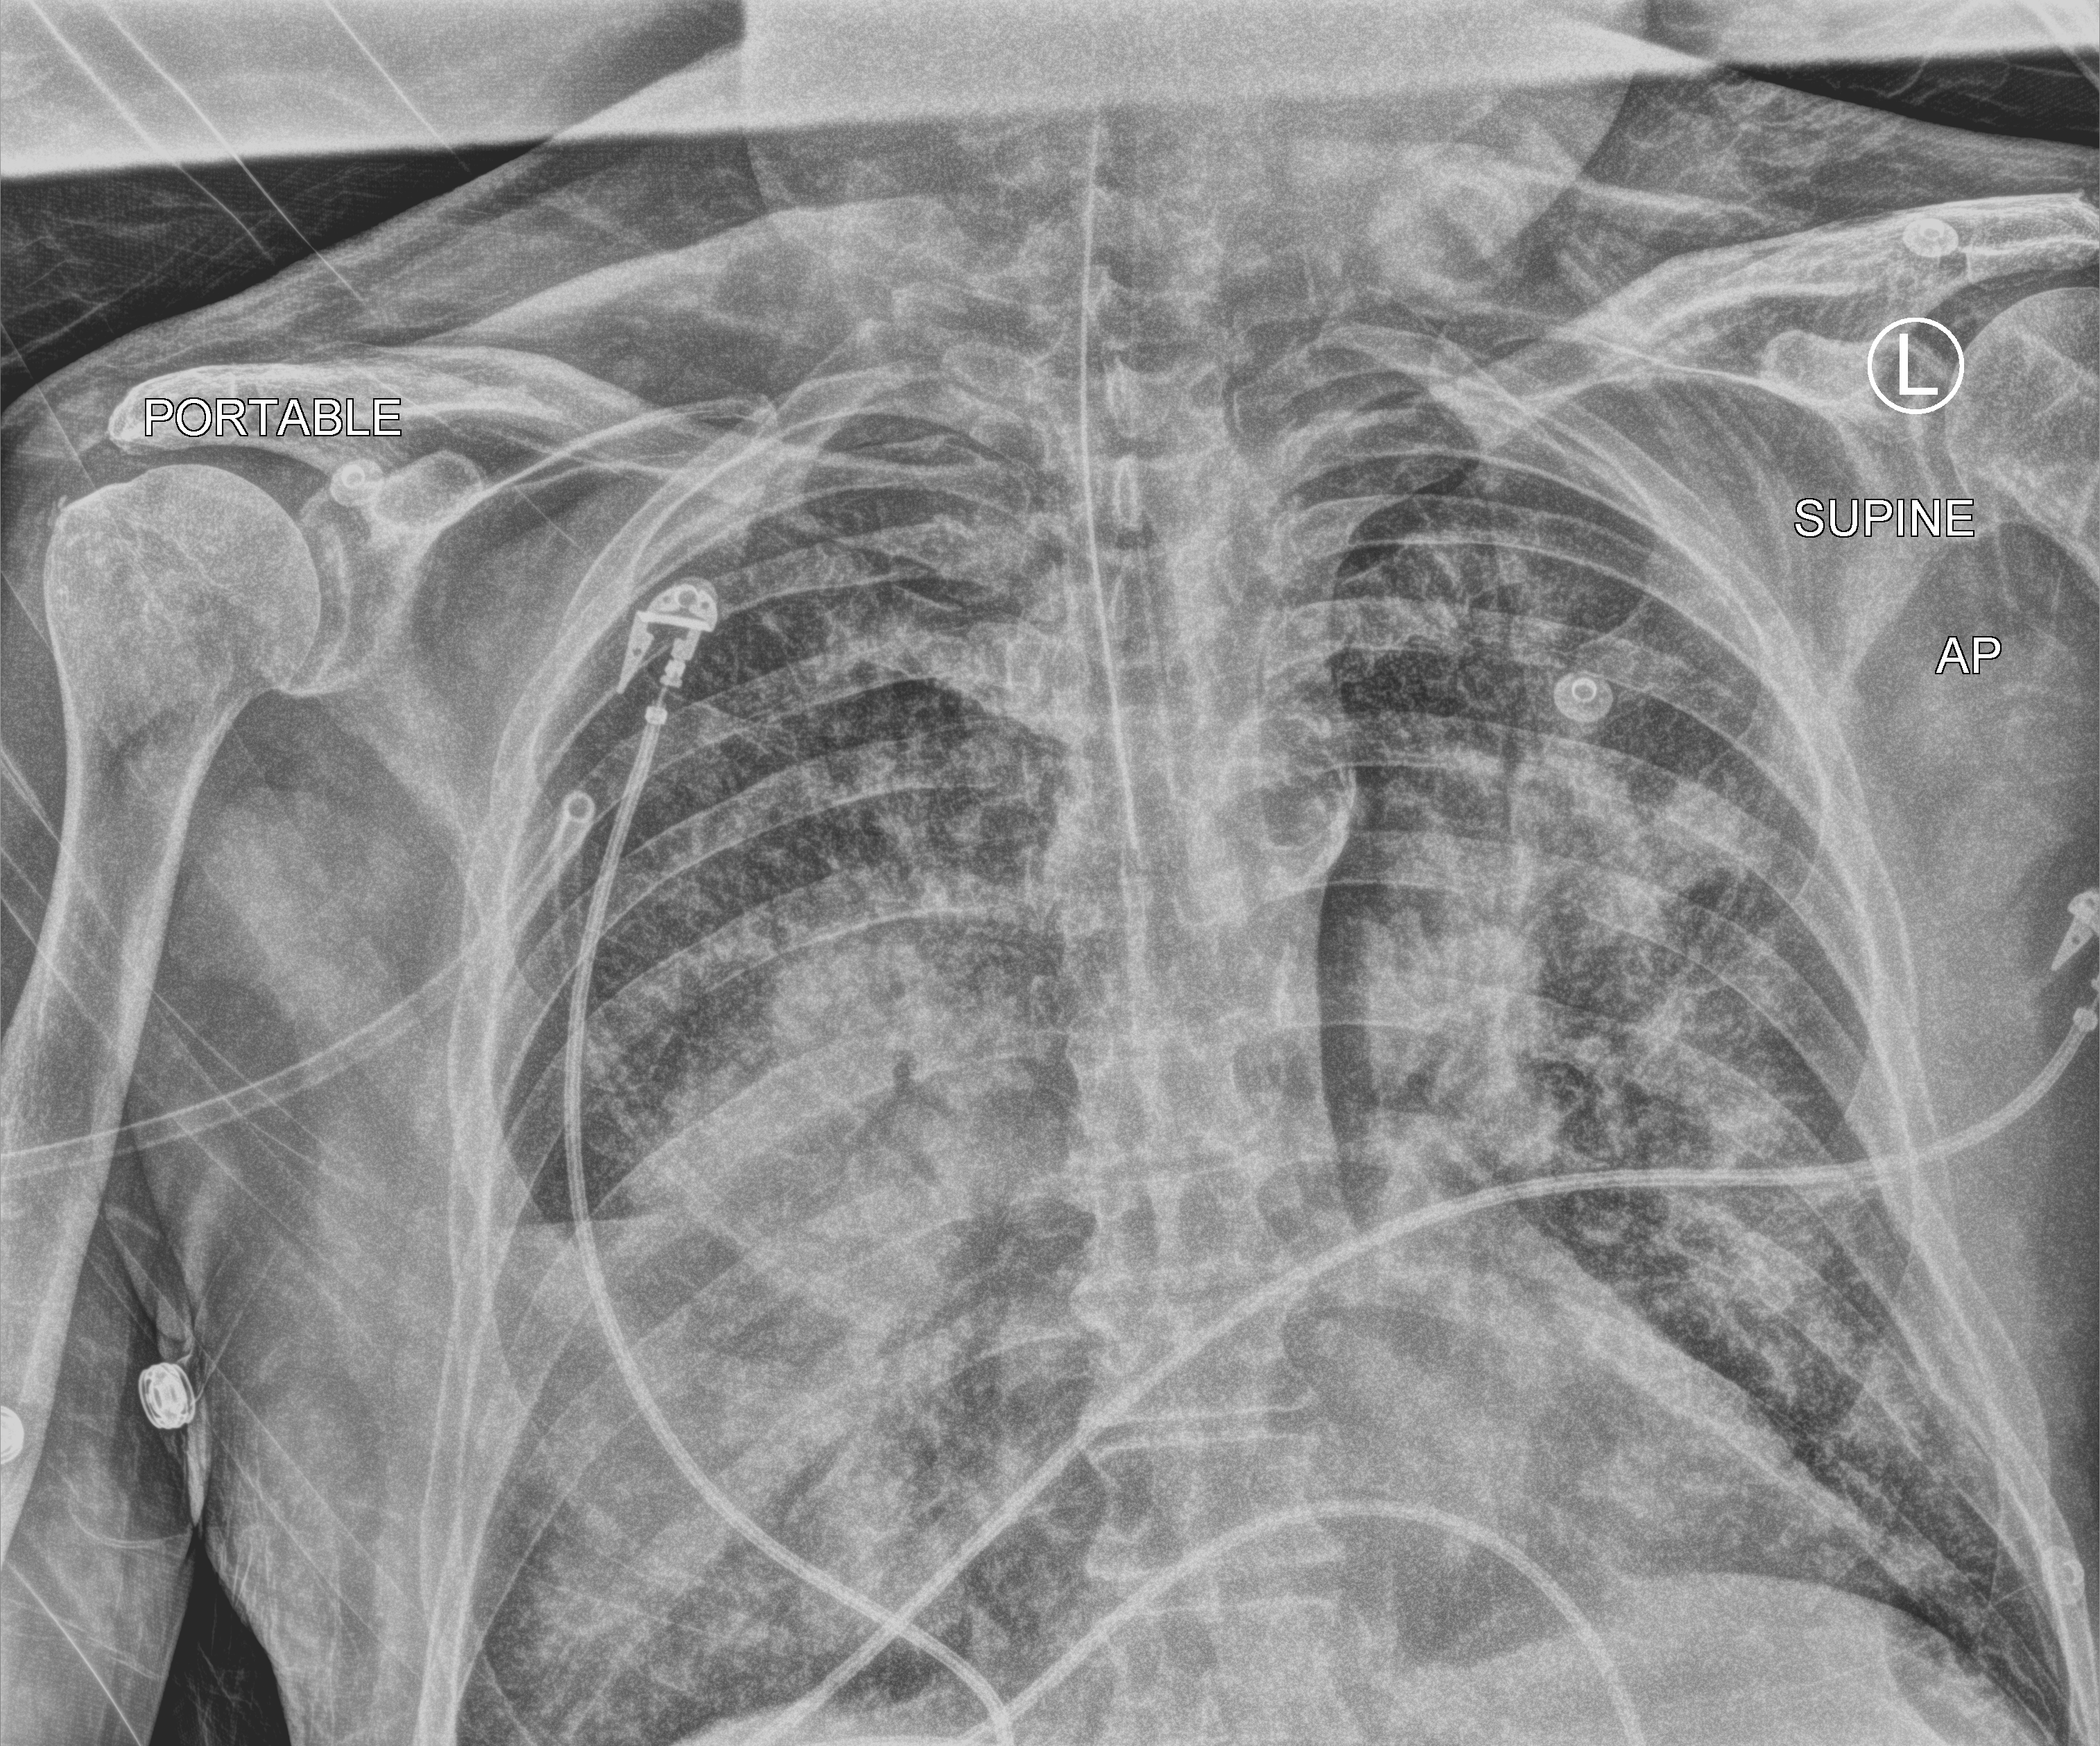
Bedside chest radiograph (computed radiography), anteroposterior (AP) projection. Male patient hospitalised with COVID-19, age 60–74 years.
Admission-level facts for this patient (not findings on this image; timing relative to this image not recorded):
- length of hospital stay: 6 days
- mechanically ventilated during this hospital stay: yes